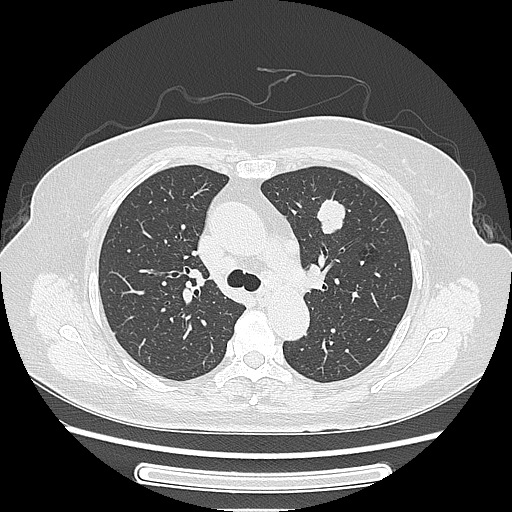
Chest CT, one axial slice. Position 163 of 227 along the scan axis. Reconstruction kernel LUNG. Lung window (W 1500 / L -600 HU). 1.25 mm slice thickness. 512 × 512 image matrix, field of view 363 × 363 mm. Female patient, age 77 years. From the clinical record (not read from this slice): clinical TNM (as recorded): T1c N3 M0; histopathological grade: G2-3.
Structures marked on this image (rectangle marked by the reading radiologist):
- lung tumour (recorded histology: adenocarcinoma): bounding box <316,192,360,250> (left, top, right, bottom; pixels)